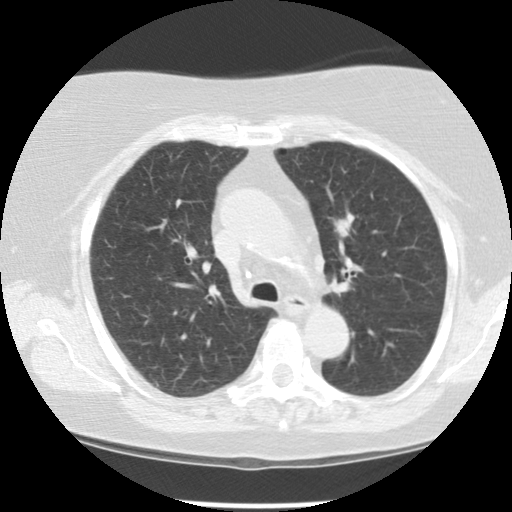
Low-dose screening chest CT, axial slice. First (baseline) screen. Lung window (W 1500 / L -600 HU). 2.5 mm slice thickness. Standard (soft-tissue) reconstruction kernel (STANDARD). Slice 33 of 108 in the series. 512 × 512 image matrix. Female, age 67 years at enrolment. Former smoker at enrolment.
Expert-annotated lung lesion, bounding box (x1, y1, x2, y2) in pixels: (310, 203, 363, 255). Screening reader's record for this exam (one nodule recorded; not confirmed to be the boxed lesion): non-calcified nodule or mass ≥4 mm, left upper lobe, 13 × 10 mm, poorly defined margins, soft tissue attenuation. Later outcome: lung cancer diagnosed 399 days after this screen (after the second annual screen) — adenocarcinoma, NOS, left upper lobe, moderately differentiated (G2), stage IIA (AJCC 6th edition), 23 mm at pathology.